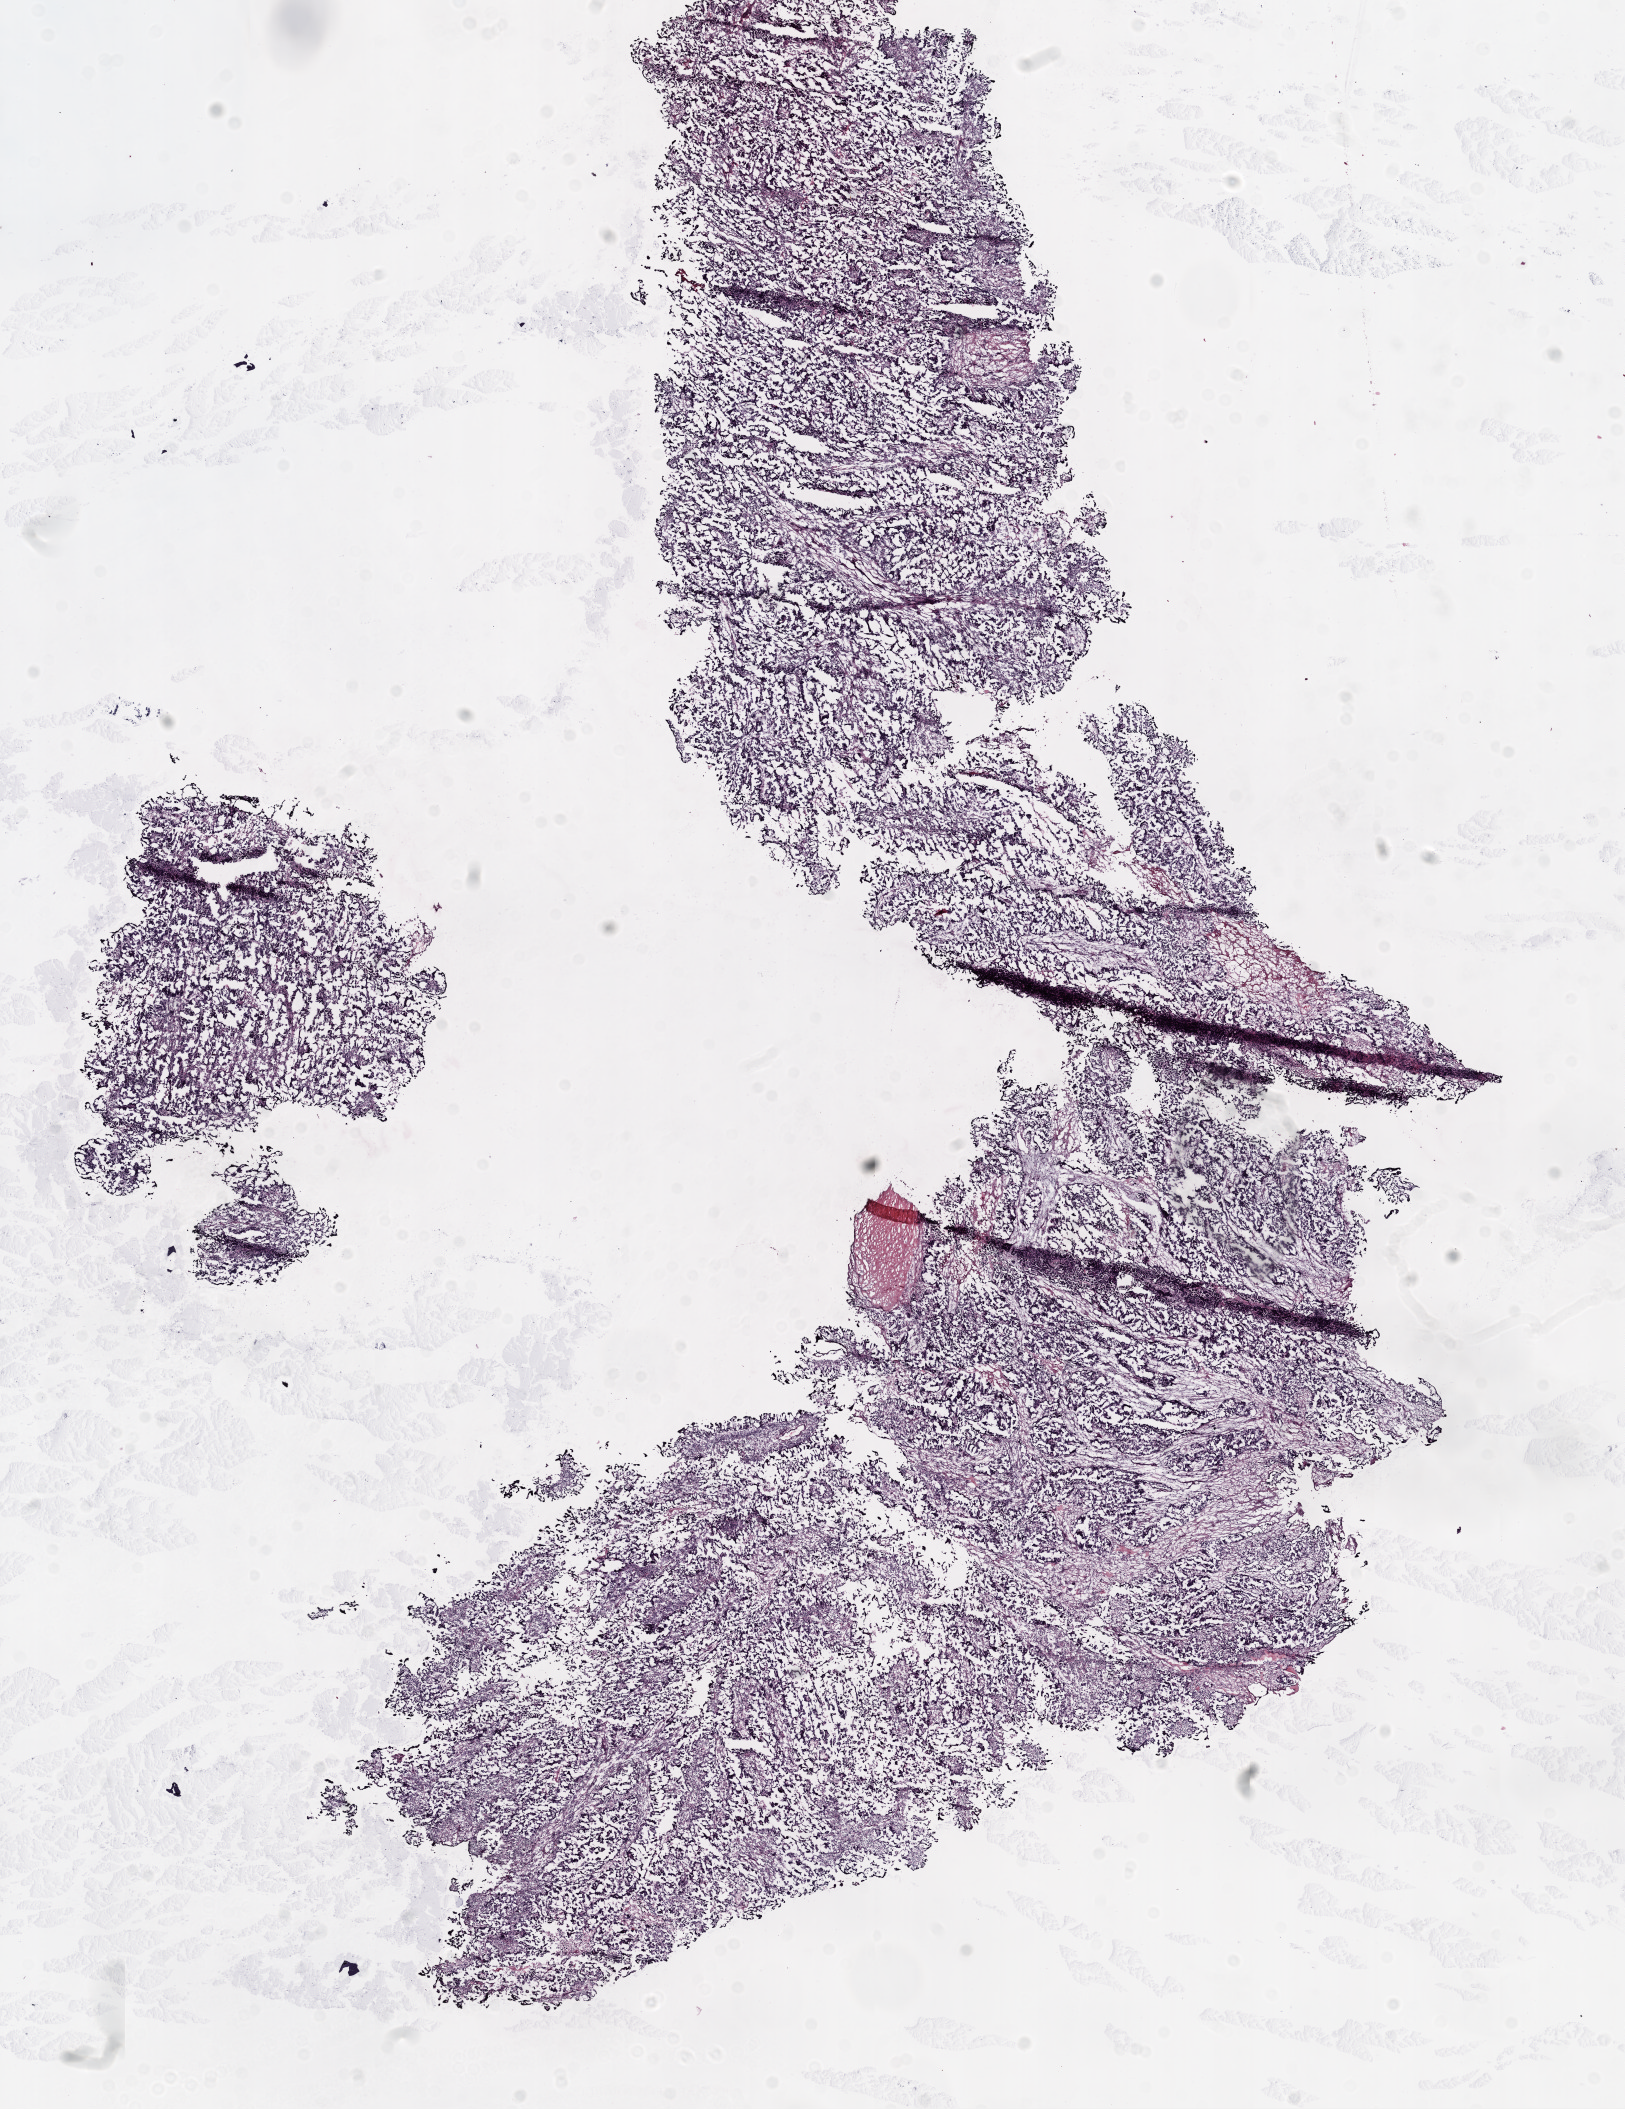
H&E whole-slide image — whole scanned area (about 13.0 x 16.9 mm) shown as a low-resolution overview; frozen section; primary tumour sample from the ovary. Female patient; age at initial diagnosis 58 years. Histologic grade: G3 (poorly differentiated). Slide review estimates, as recorded: tumour cells 90%, tumour nuclei 95%, normal cells 0%, stromal cells 5%, necrosis 5%.
Histologic diagnosis: Serous cystadenocarcinoma, NOS. FIGO stage: IIIC.